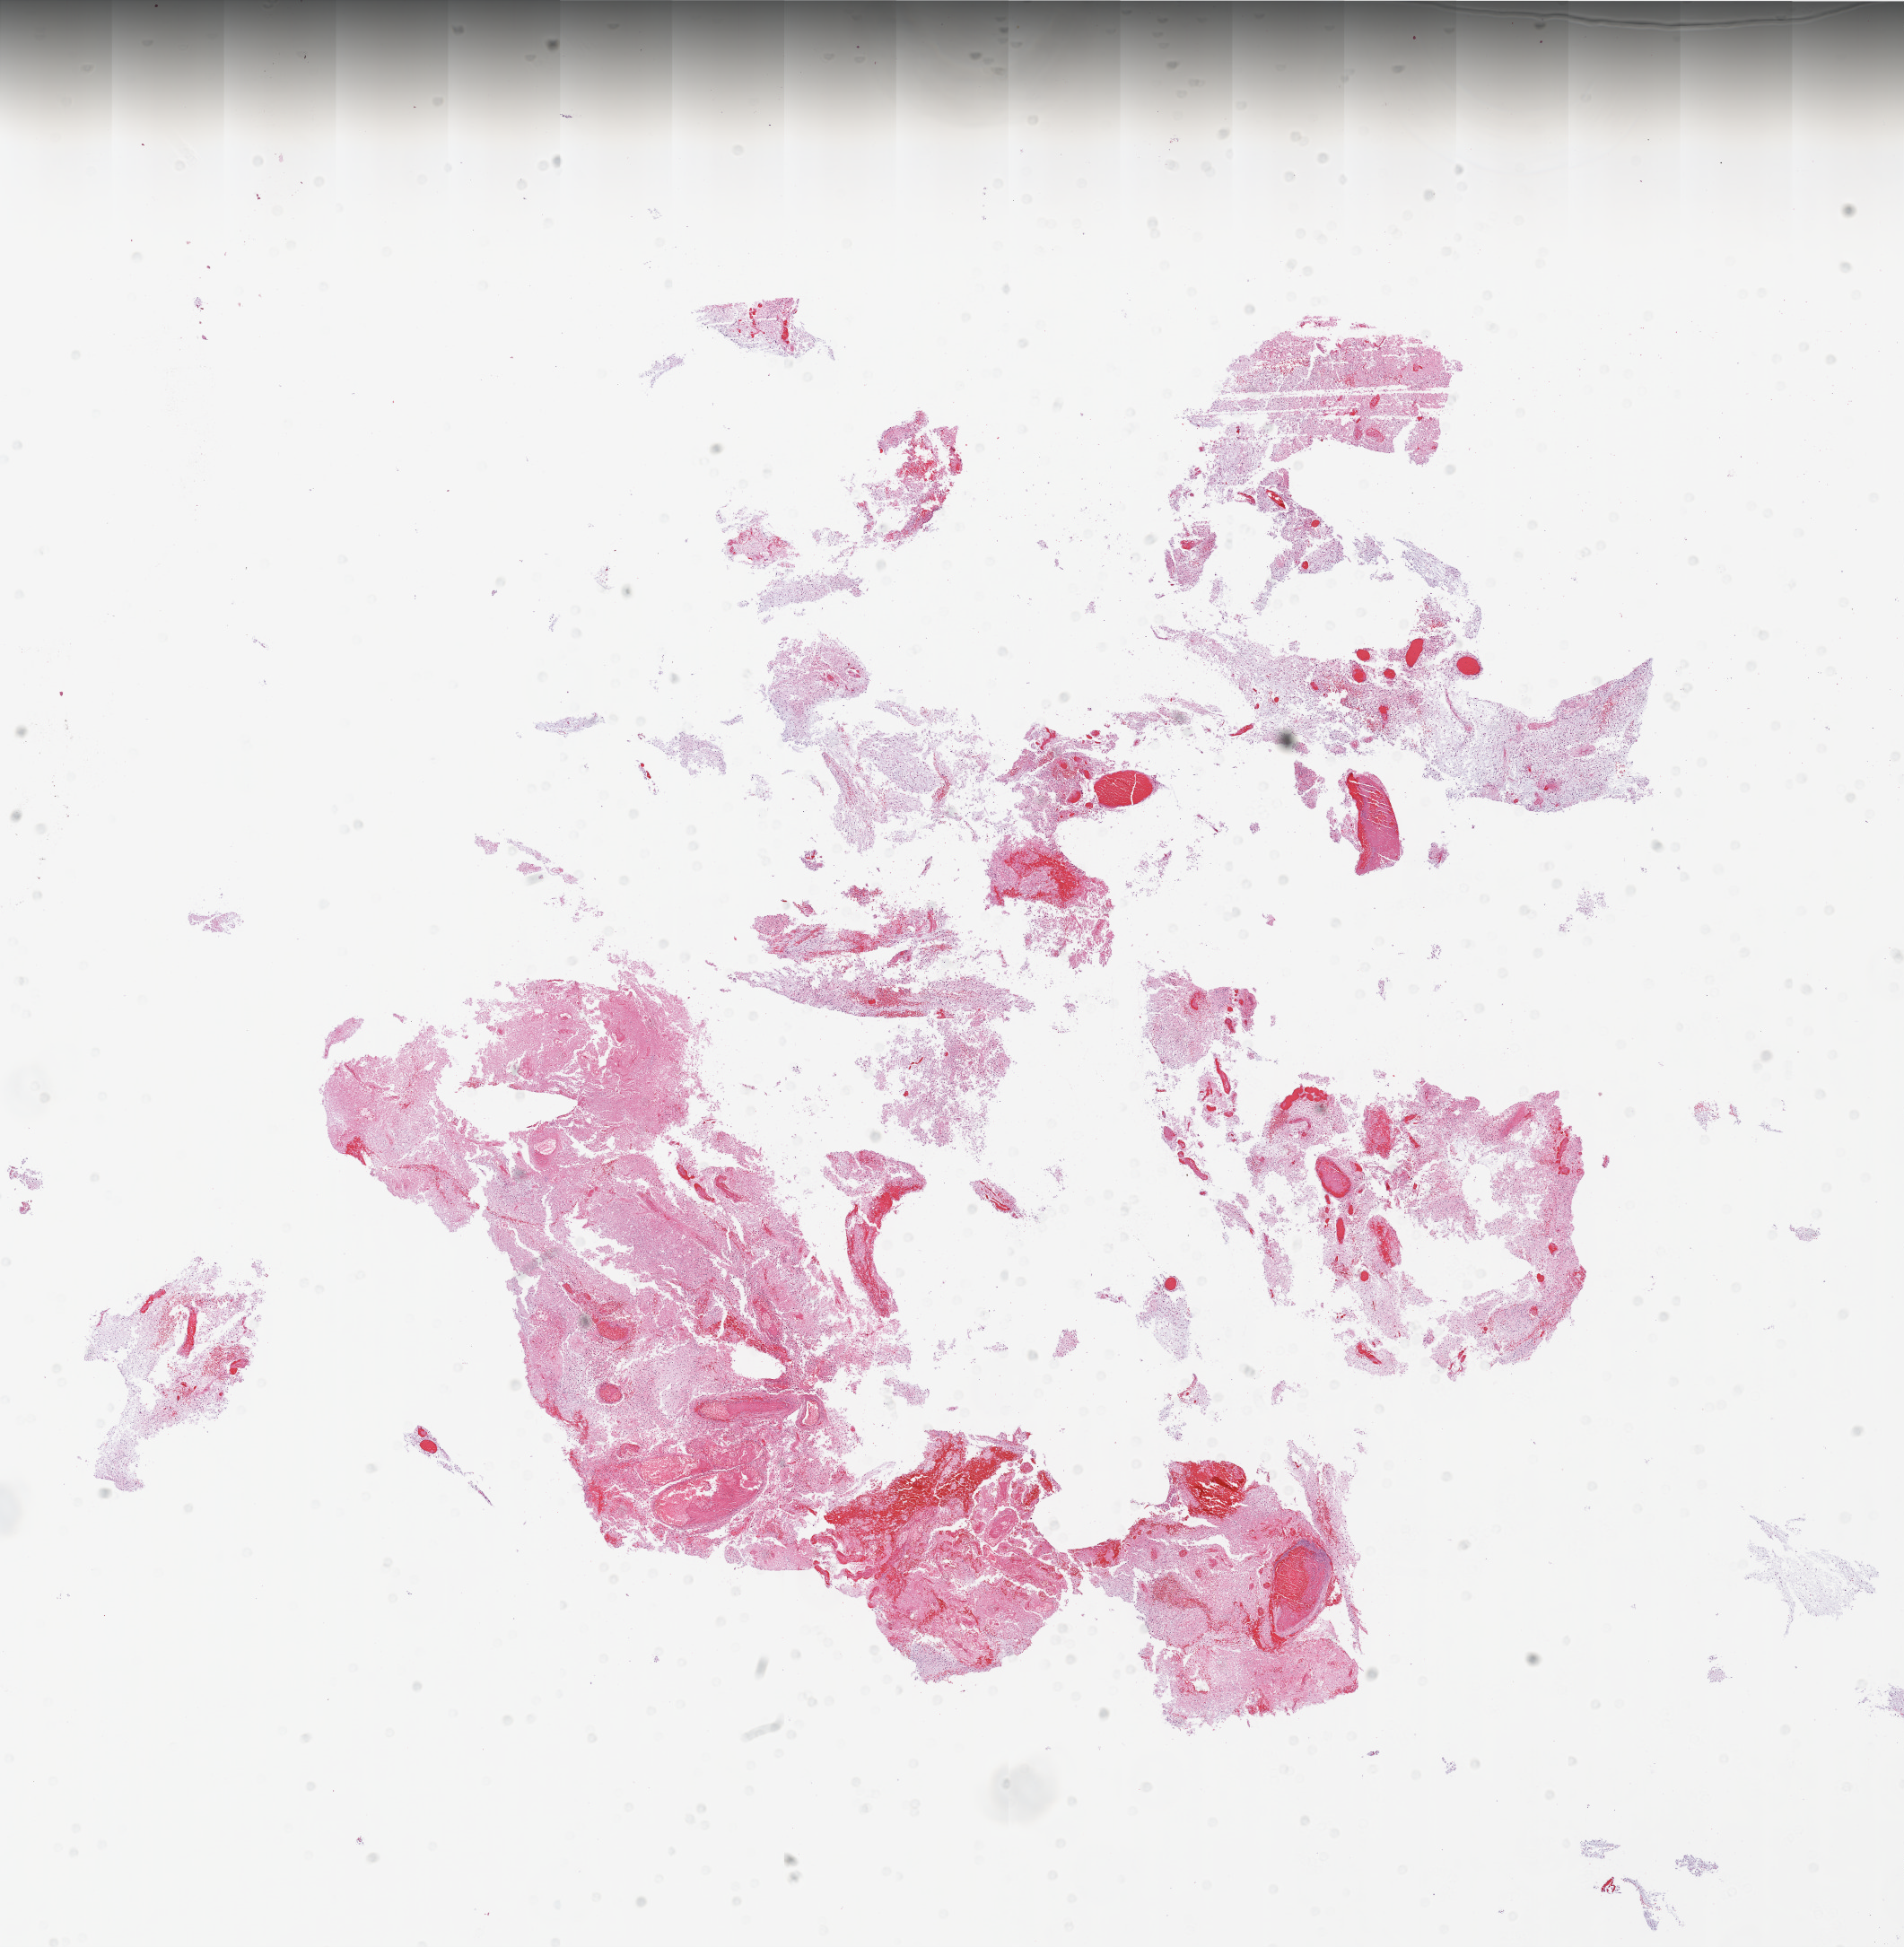
H&E-stained whole-slide image, shown as a low-resolution overview of the whole scanned area (about 17.0 x 17.4 mm, acquisition: 20x scan); formalin-fixed paraffin-embedded (FFPE) diagnostic section; sample: primary tumour, brain. Female, age 51 years at initial diagnosis.
Histologic diagnosis: Glioblastoma.